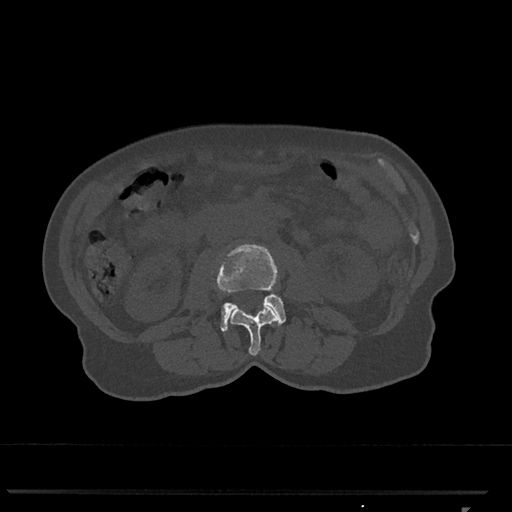
CT including the spine, one axial slice; 120 kVp; bone window (W 1800 / L 400 HU); 0.5 mm slice thickness; 512 × 512 image matrix. Patient: female, 62 years. Case-level facts recorded for this patient, not image findings: primary cancer: renal.
Outlined on this slice (semi-automatically segmented with operator editing):
- L2 vertebra: bounding box <230,305,278,356> (left, top, right, bottom; pixels)
- L3 vertebra: <217,244,286,332>